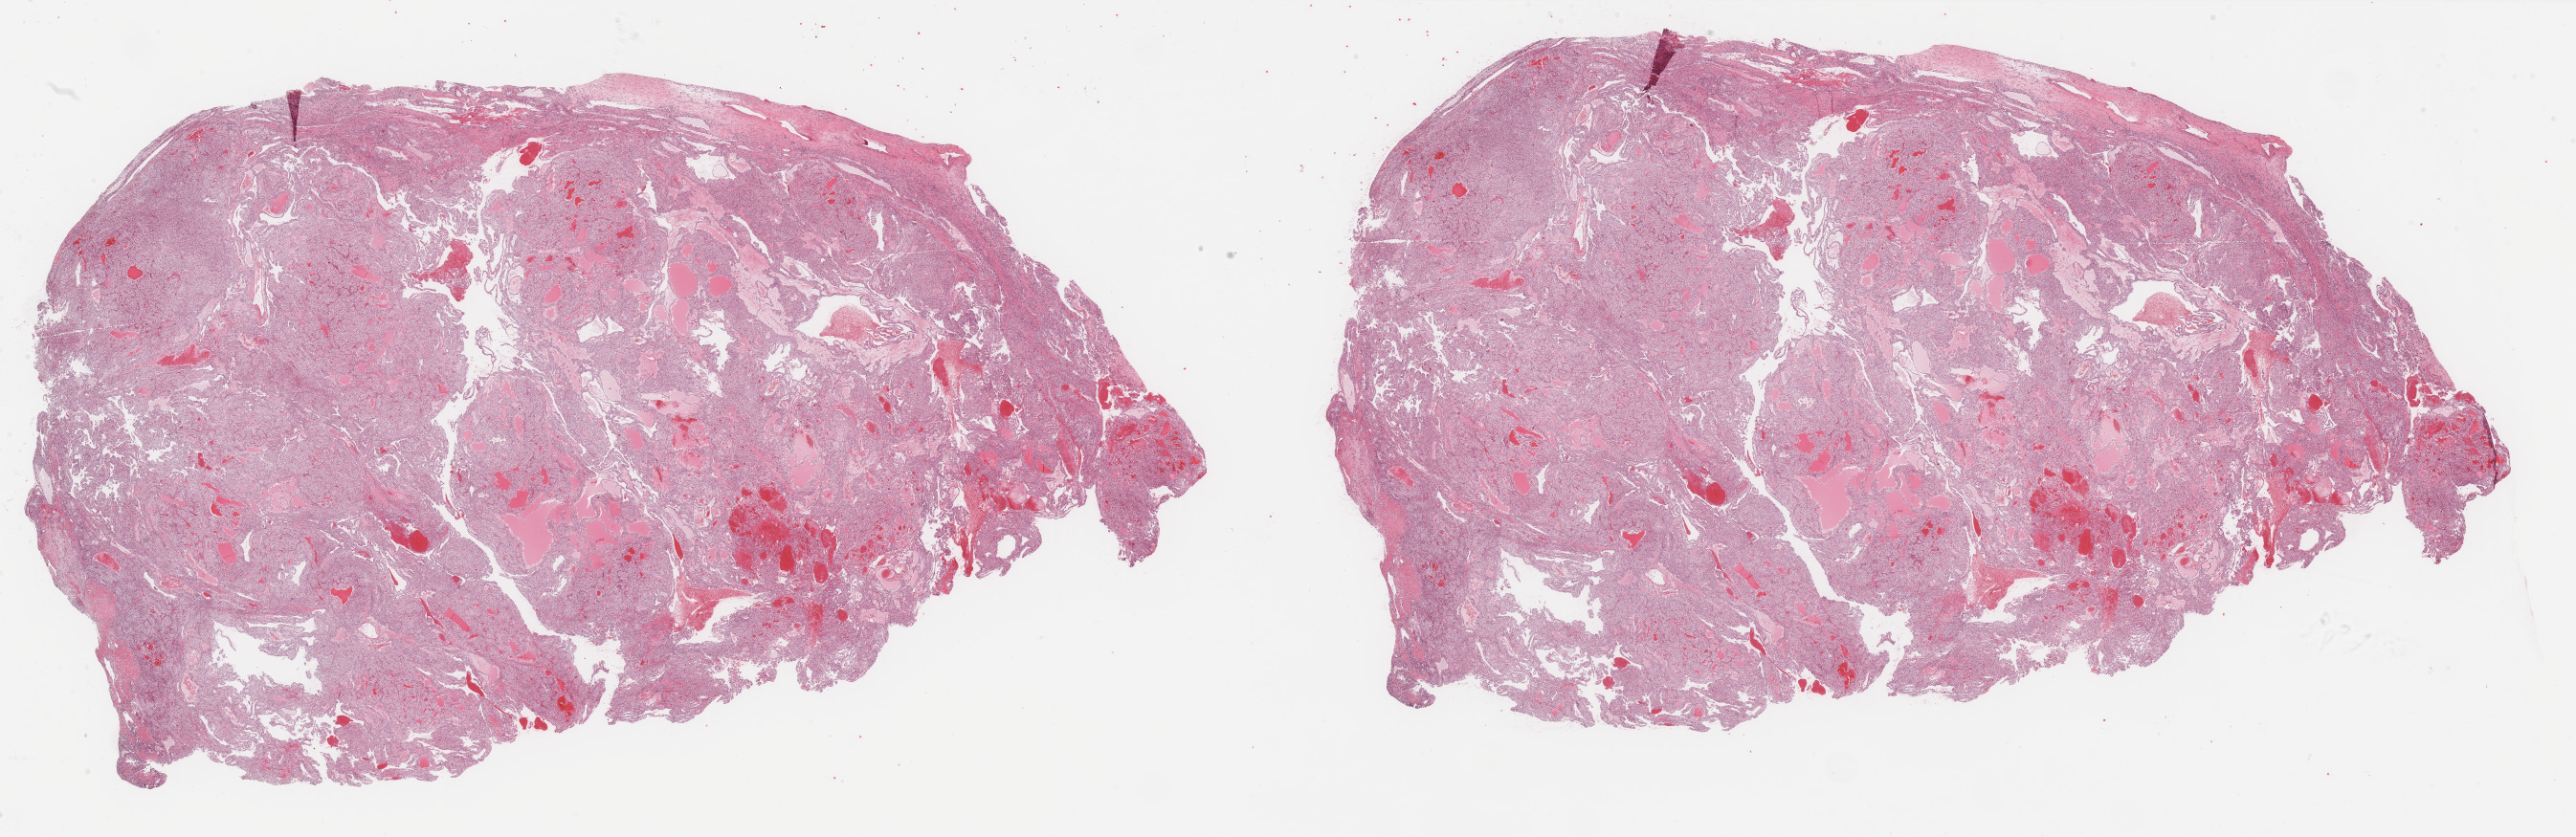
Digitized H&E tissue section (whole slide), low-resolution overview of the scanned area, about 42.6 x 13.8 mm (acquisition: 40x scan), formalin-fixed paraffin-embedded (FFPE) diagnostic section, sample: primary tumour, kidney. Patient: female, age at initial diagnosis 49 years. Histologic grade: G2 (moderately differentiated).
Pathologic diagnosis: Renal cell carcinoma, NOS. AJCC pathologic stage: I (7th edition). Laterality: left.